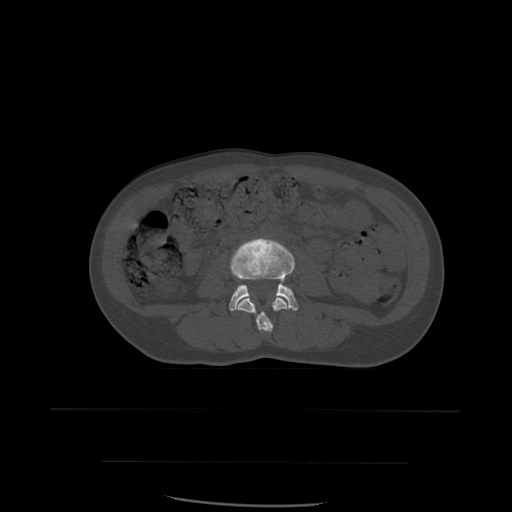
CT including the spine, one axial slice. Bone window (W 1800 / L 400 HU). 512 × 512 image matrix, field of view 392 × 392 mm. Patient age 48 years. Case-level facts recorded for this patient, not image findings: primary cancer: lung; vertebrae with lytic lesions (as recorded): T11.
Annotated regions visible in this slice (semi-automatically segmented with operator editing):
- L3 vertebra: bounding box [x1, y1, x2, y2] px = [237, 298, 288, 333]
- L4 vertebra: [229, 239, 299, 312]